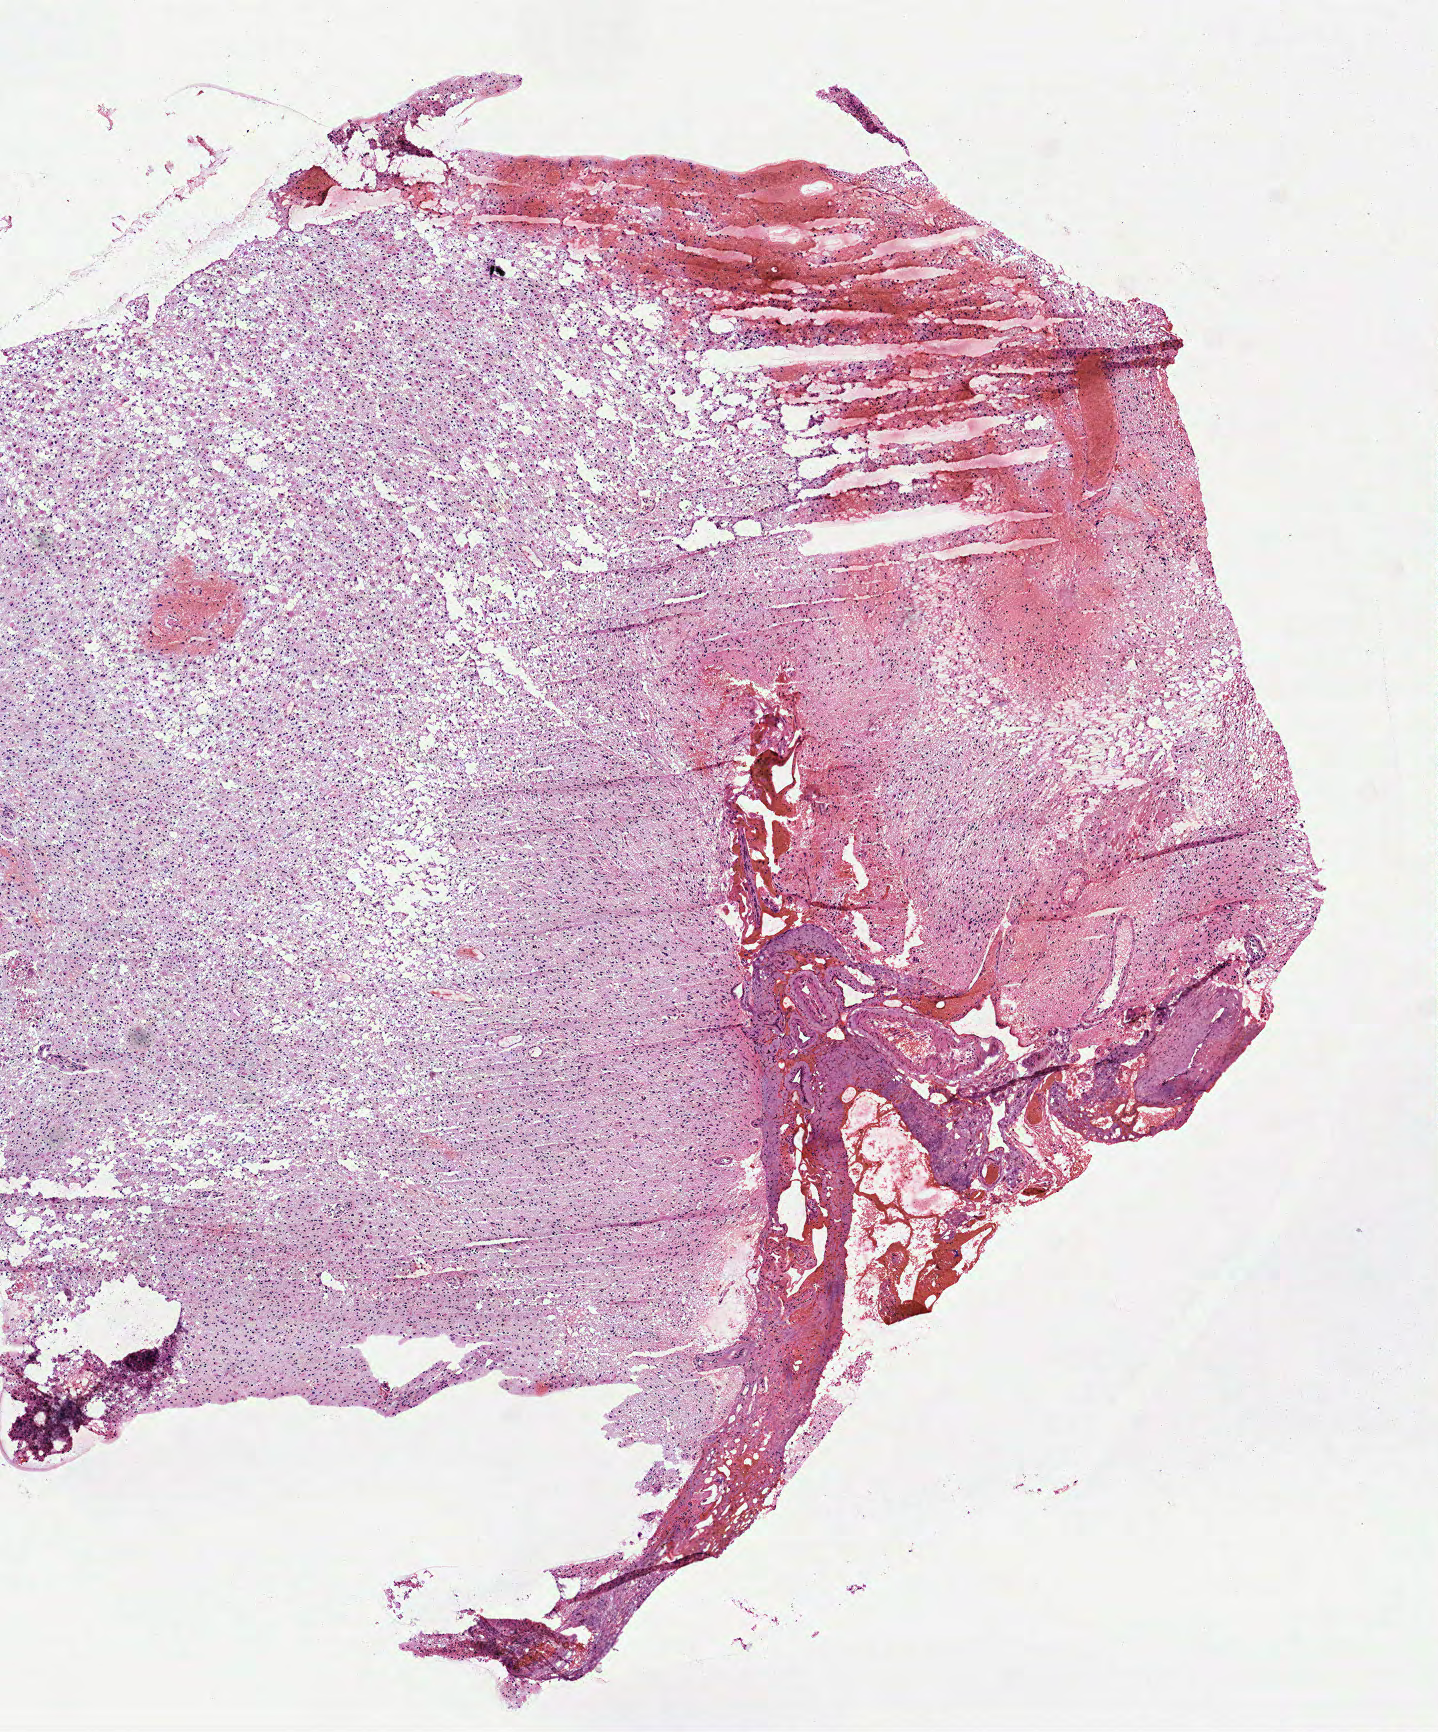
Hematoxylin and eosin (H&E) stained whole-slide image — whole scanned area (about 5.8 x 7.0 mm) shown as a low-resolution overview; frozen section; sample: primary tumour, brain. Male, age 36 years at initial diagnosis. Histologic grade: G2 (moderately differentiated). Pathologist review of this section (percent, as recorded): tumour cells 100%, tumour nuclei 75%, normal cells 0%, stromal cells 0%, necrosis 0%.
Diagnosis: Astrocytoma, NOS (cerebrum).